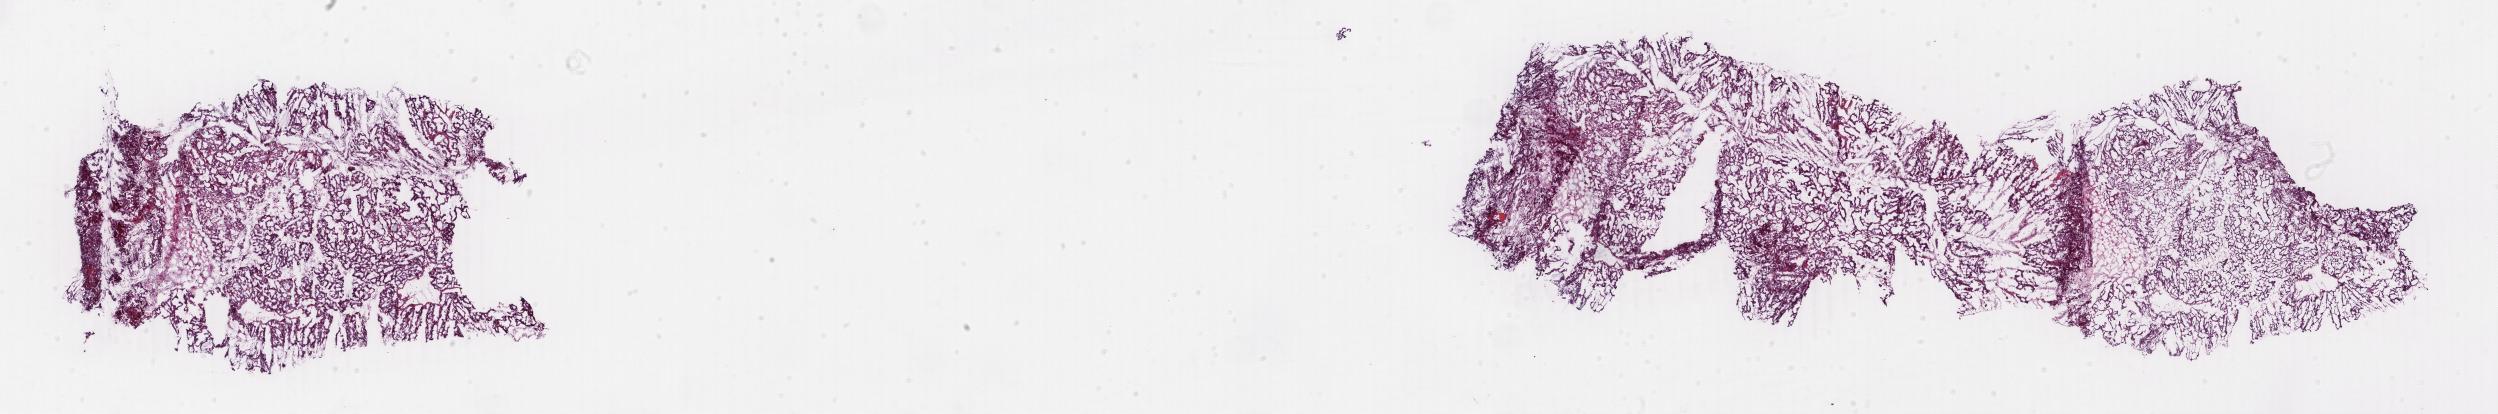
Whole-slide histology image, H&E-stained, shown as a low-resolution overview of the whole scanned area (about 39.7 x 6.6 mm, slide scanned at 40x), frozen section from the top of the tissue portion, uterus, primary tumour sample. Patient: female, age at initial diagnosis 77 years. Histologic grade: G3 (poorly differentiated). Slide review estimates, as recorded: tumour cells 80%, tumour nuclei 95%, normal cells 3%, stromal cells 2%, necrosis 15%. Infiltration values recorded for this section: lymphocyte infiltration 1%, monocyte infiltration 0%, neutrophil infiltration 0%.
FIGO stage: IC. Diagnosis: Endometrioid adenocarcinoma, NOS (endometrium).